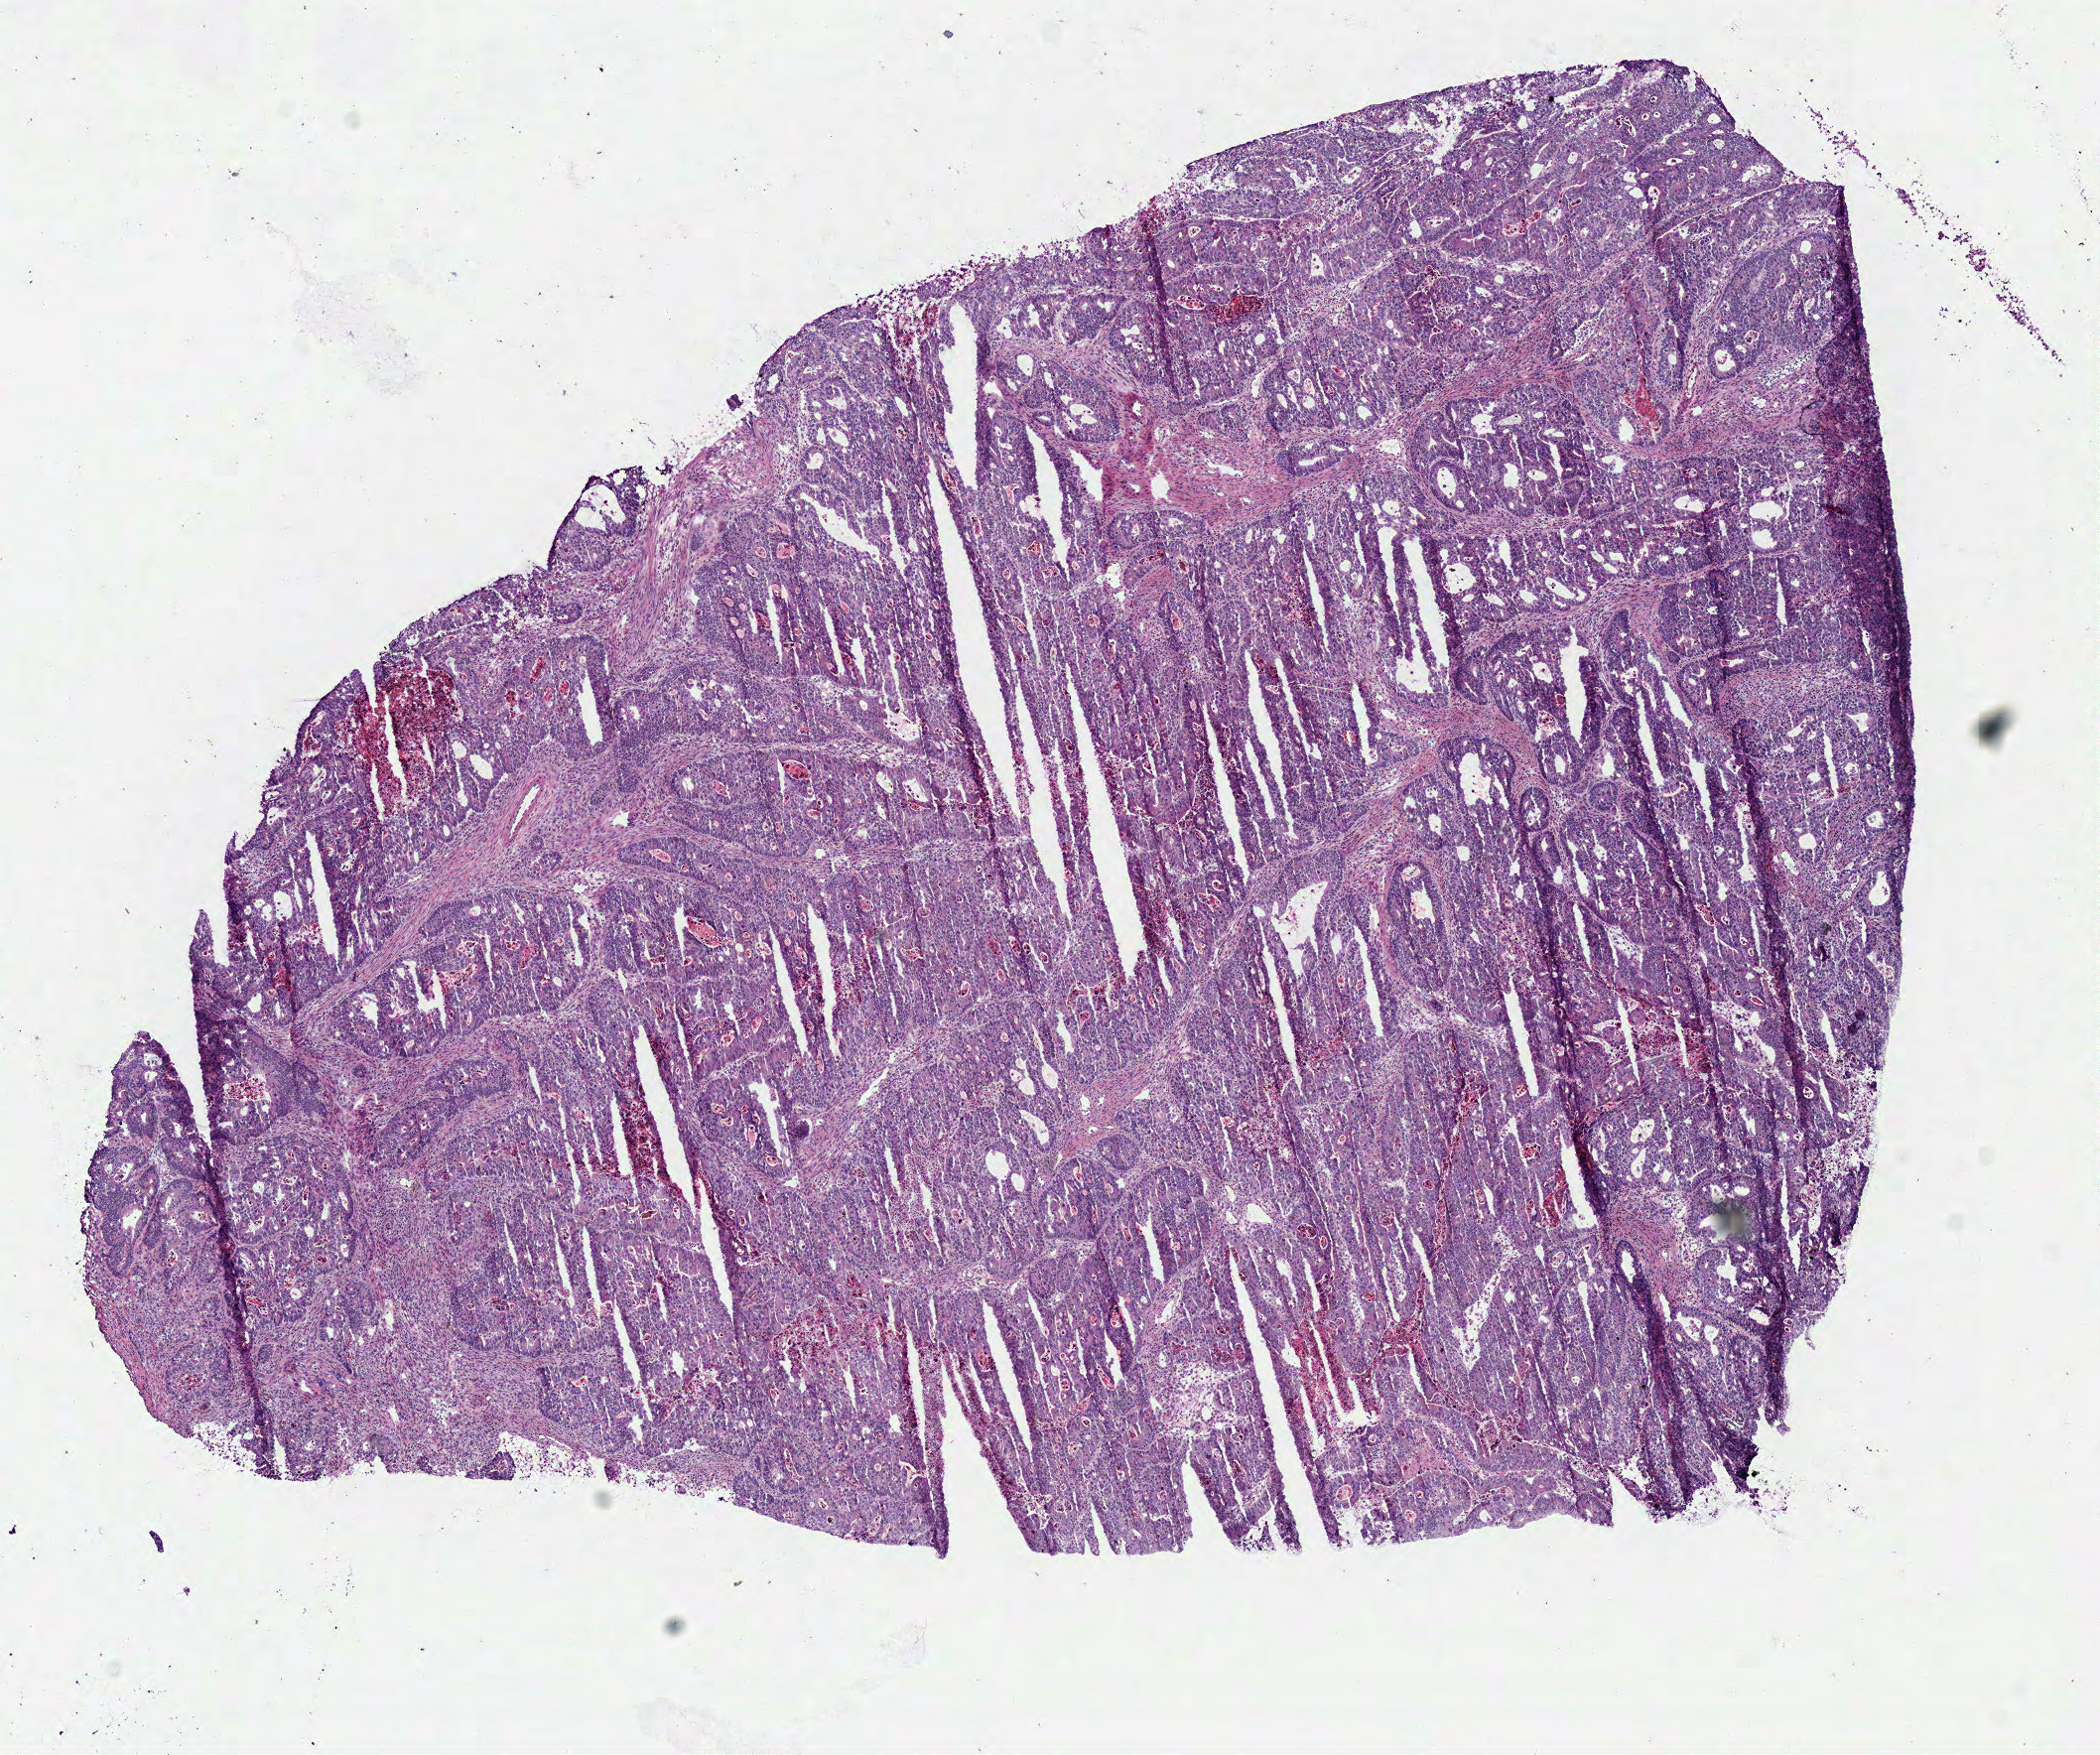
Whole-slide histology image, H&E-stained, low-resolution overview of the scanned area, about 8.3 x 7.0 mm (slide scanned at 40x). Frozen section. Primary tumour sample from the rectum. Female patient; age at initial diagnosis 64 years. Slide review estimates, as recorded: tumour cells 75%, tumour nuclei 80%, normal cells 0%, stromal cells 10%, necrosis 15%.
- pathologic diagnosis: Adenocarcinoma in tubulovillous adenoma
- AJCC pathologic stage: IIIB (7th edition)
- lymph nodes positive (case pathology): 1 of 17 examined